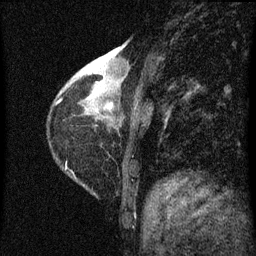
Breast MRI (dynamic contrast-enhanced), one sagittal slice. Position 16 of 60 along the scan axis. Dynamic contrast-enhanced series, image 2 of 3 at this slice position (ordered by acquisition). 1.5 T. TE 4.2 ms, TR 8 ms. 2 mm slice thickness. 256 × 256 image matrix, field of view 180 × 180 mm. Female patient, age 38 years.
Outlined on this slice (semi-automatic segmentation, software-assisted and operator-edited):
- analysis volume of interest (the breast-tissue region the enhancement analysis was run in; not a lesion): box from (x=67, y=42) to (x=144, y=131) px
- tumour enhancement mask (voxels above the 70 % enhancement threshold inside the analysis volume of interest): (x=88, y=72)–(x=113, y=111)